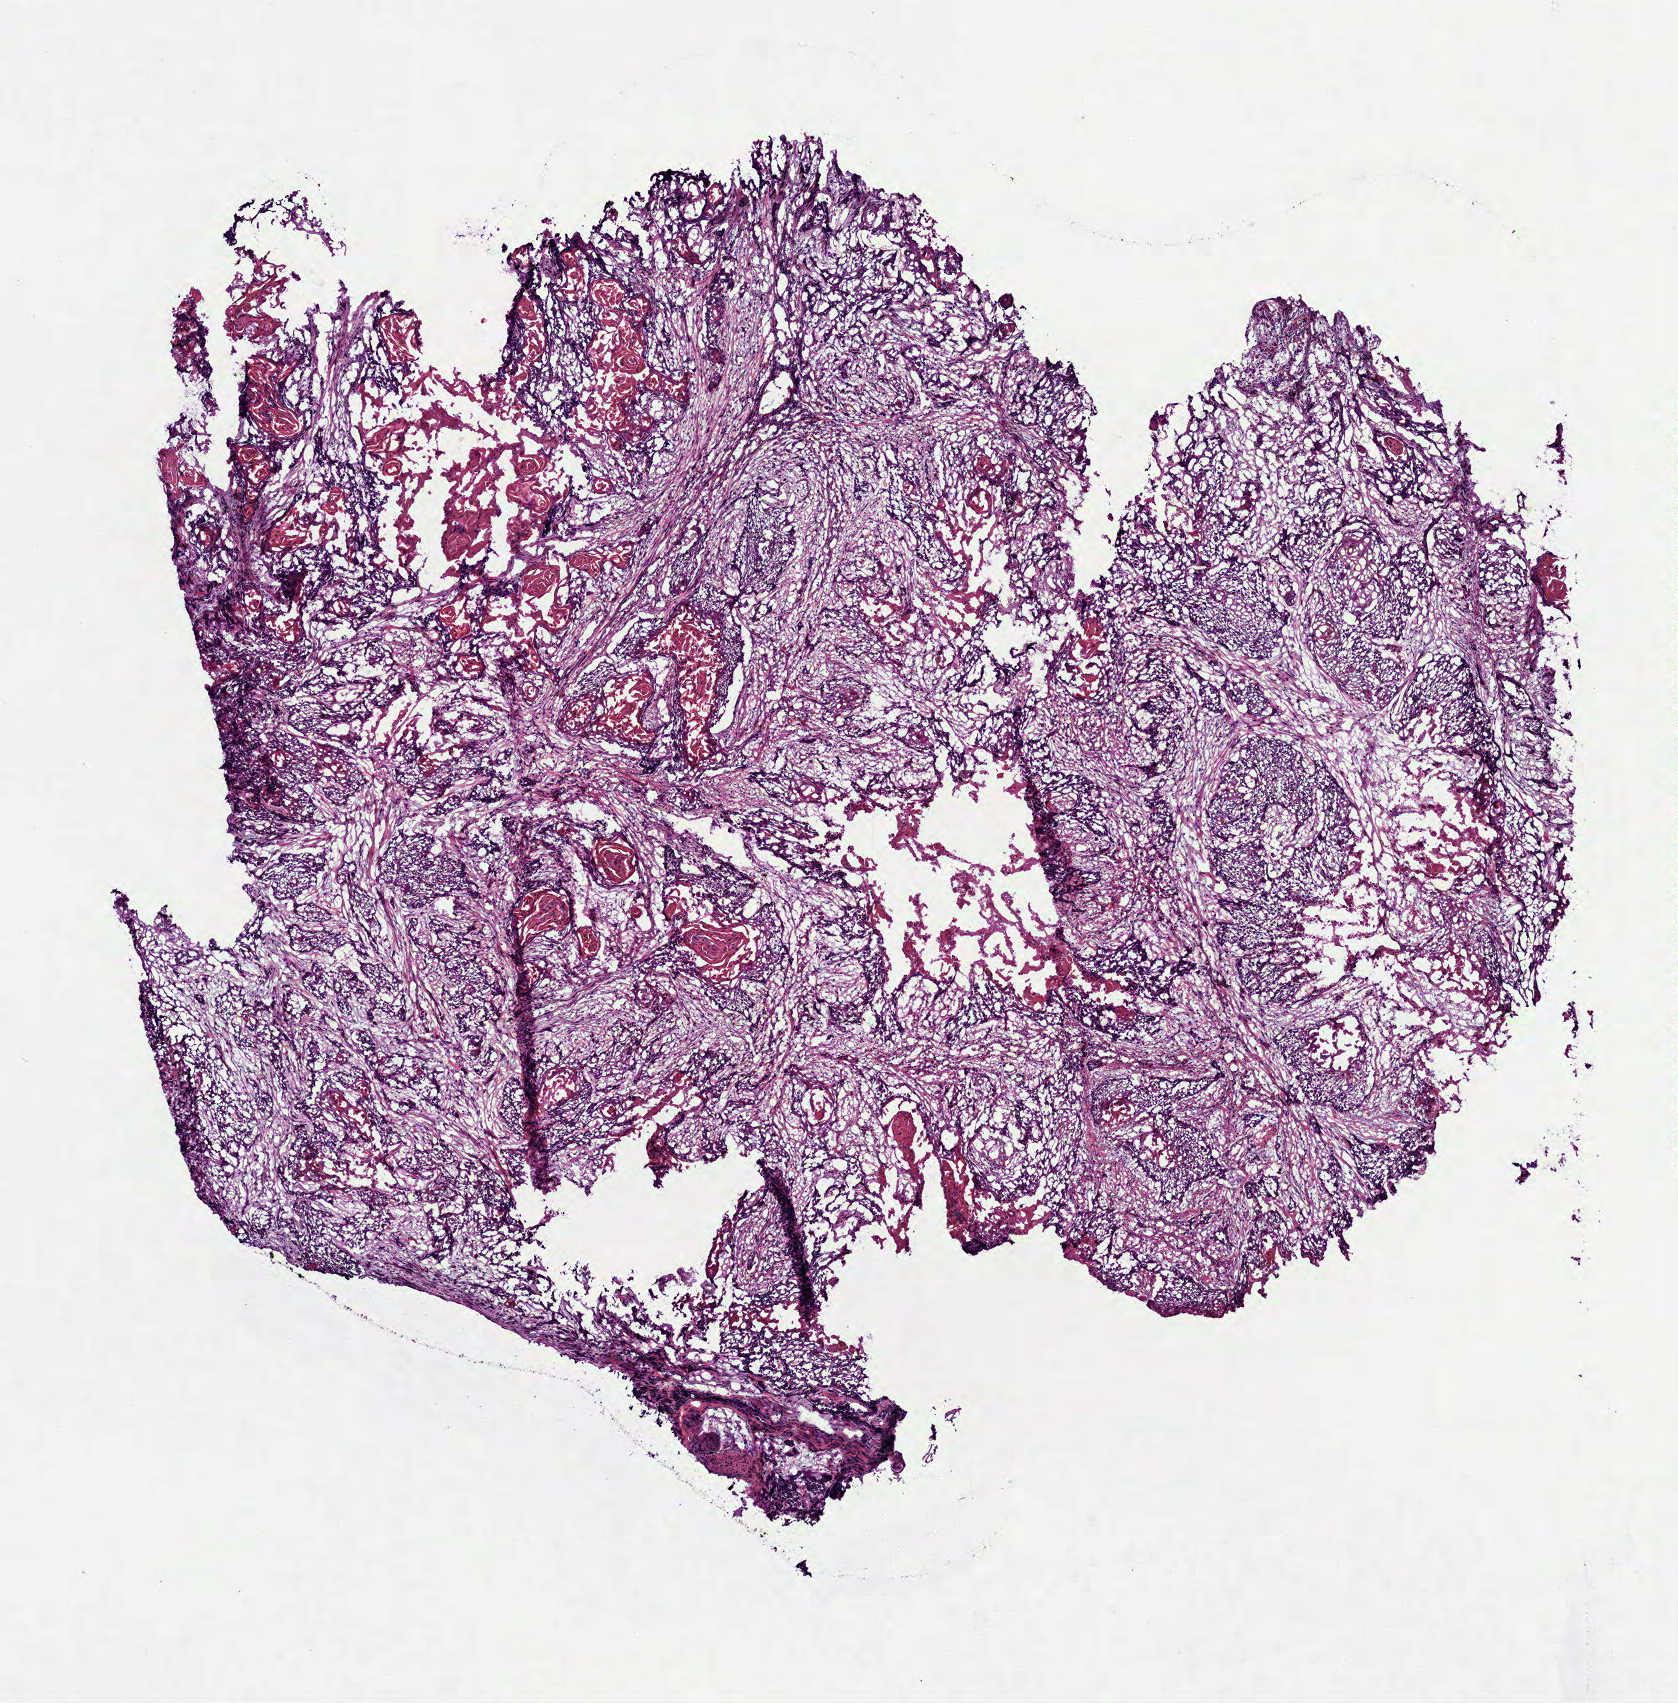
Whole-slide histology image, H&E-stained, low-resolution overview of the scanned area, about 6.8 x 6.9 mm. Frozen section. Sample: primary tumour, head and neck. Male, age 66 years at initial diagnosis. Histologic grade: G2 (moderately differentiated). Slide review estimates, as recorded: tumour cells 75%, tumour nuclei 75%, normal cells 0%, stromal cells 20%, necrosis 5%.
Histologic diagnosis: Squamous cell carcinoma, NOS (tongue, NOS). AJCC pathologic stage: IVA (6th edition).